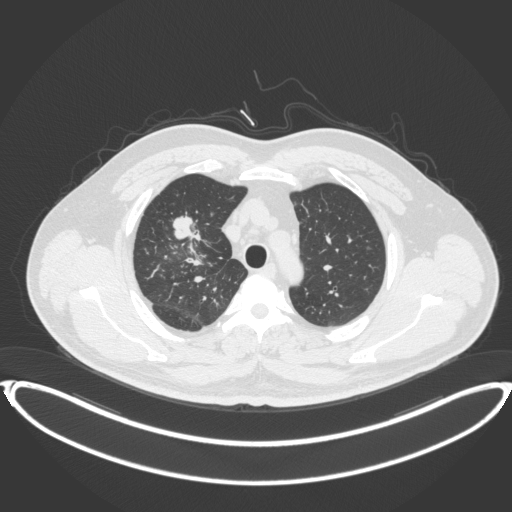
Chest CT, one axial slice. Position 302 of 399 along the scan axis. Reconstruction kernel B31f. Lung window (W 1500 / L -600 HU). 1 mm slice thickness. 512 × 512 image matrix, field of view 445 × 445 mm. Male patient, age 53 years. From the clinical record (not read from this slice): clinical TNM (as recorded): T2a N0 M0.
Annotated regions visible in this slice (bounding box drawn by a radiologist):
- lung tumour (recorded histology: adenocarcinoma): bounding box <168,209,206,249> (left, top, right, bottom; pixels)